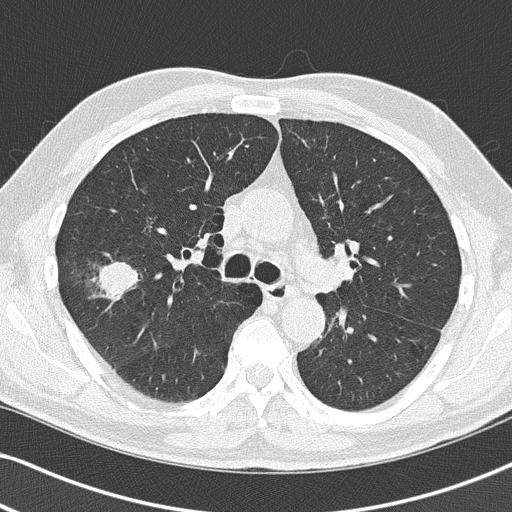
Axial slice from a low-dose chest CT screening exam; baseline screening round; lung window (W 1500 / L -600 HU); 2 mm slice thickness; lung (sharp) reconstruction kernel (B50f); 120 kVp. Male participant, aged 67 years at enrolment.
Lesion marked by an expert reader, bounding box [x1, y1, x2, y2] px = [72, 254, 148, 317]. Screening reader's record for this exam (one nodule recorded; not confirmed to be the boxed lesion): non-calcified nodule or mass ≥4 mm, right upper lobe, 26 × 24 mm, spiculated (stellate) margins, soft tissue attenuation. Official screen result: positive, change unspecified: nodule(s) >= 4 mm or enlarging nodule(s), mass(es), or other non-specific abnormalities suspicious for lung cancer. Lung cancer was diagnosed 49 days after this screen: squamous cell carcinoma, NOS, right upper lobe, poorly differentiated (G3), stage IA (AJCC 6th edition), 27 mm at pathology.